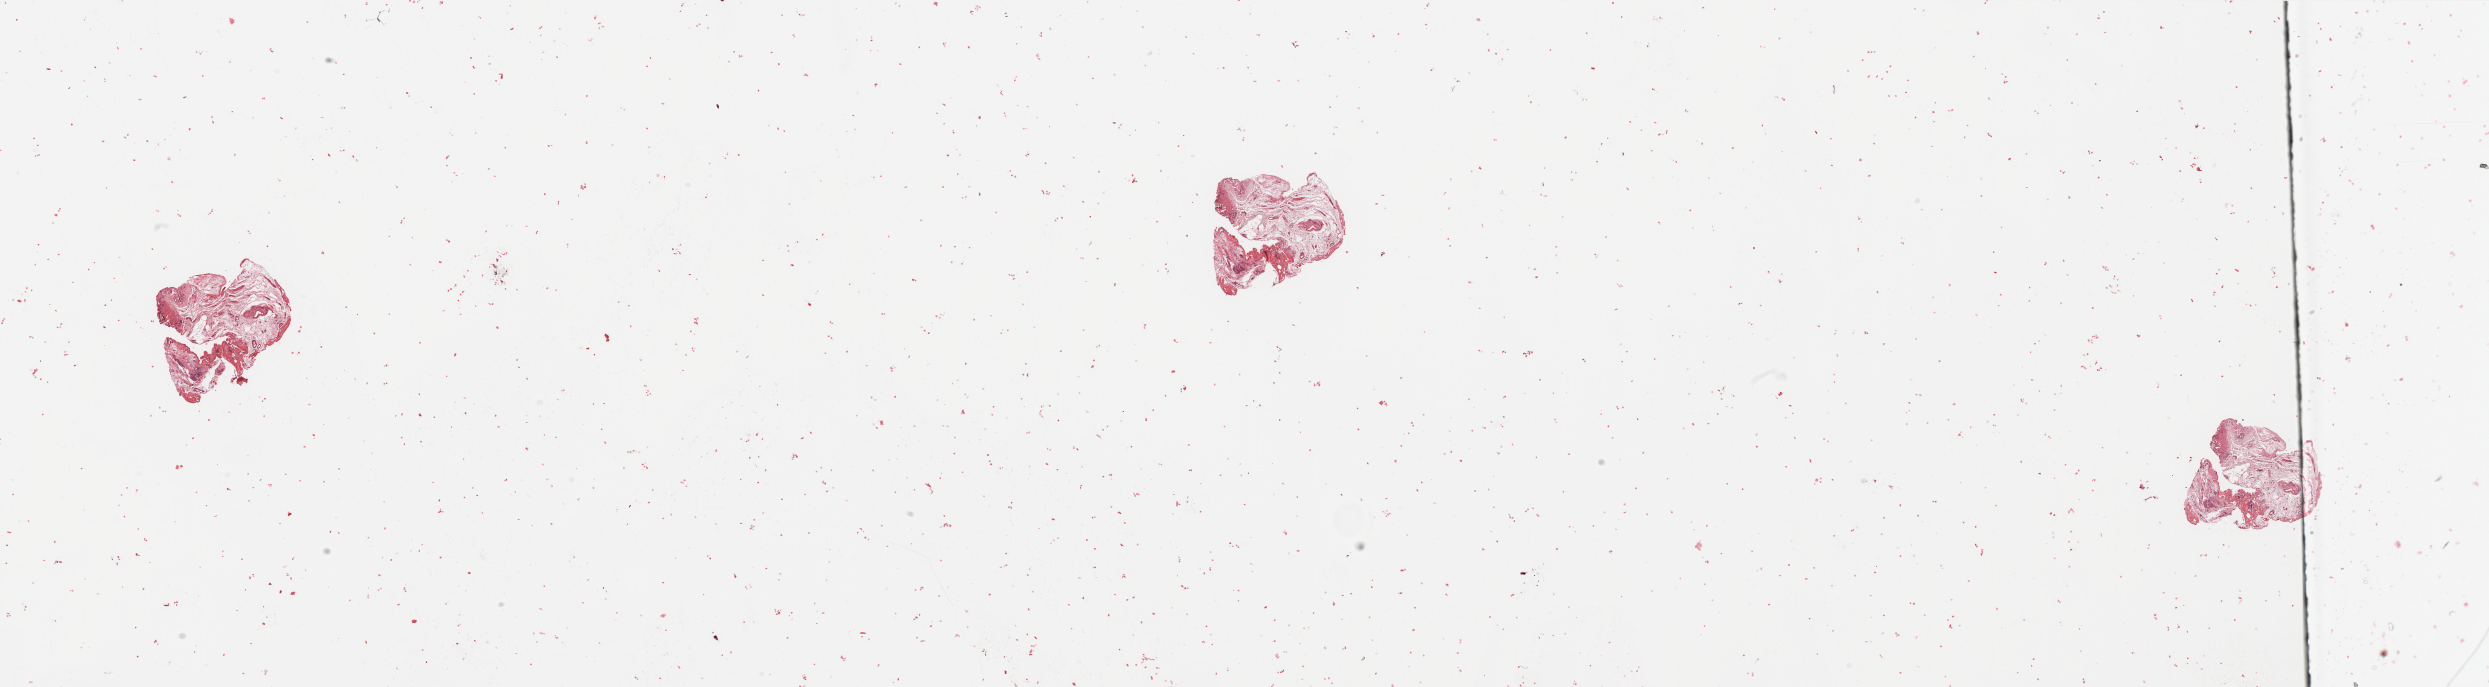
Digitized H&E tissue section (whole slide) — shown as a low-resolution overview of the whole scanned area (about 39.4 x 10.9 mm, slide scanned at 20x). Normal (non-tumour) tissue sample, sampled site: pancreas. Female, 63 y/o.
This section: normal (non-tumour) tissue from the same patient. Patient diagnosis: Infiltrating duct carcinoma, NOS.